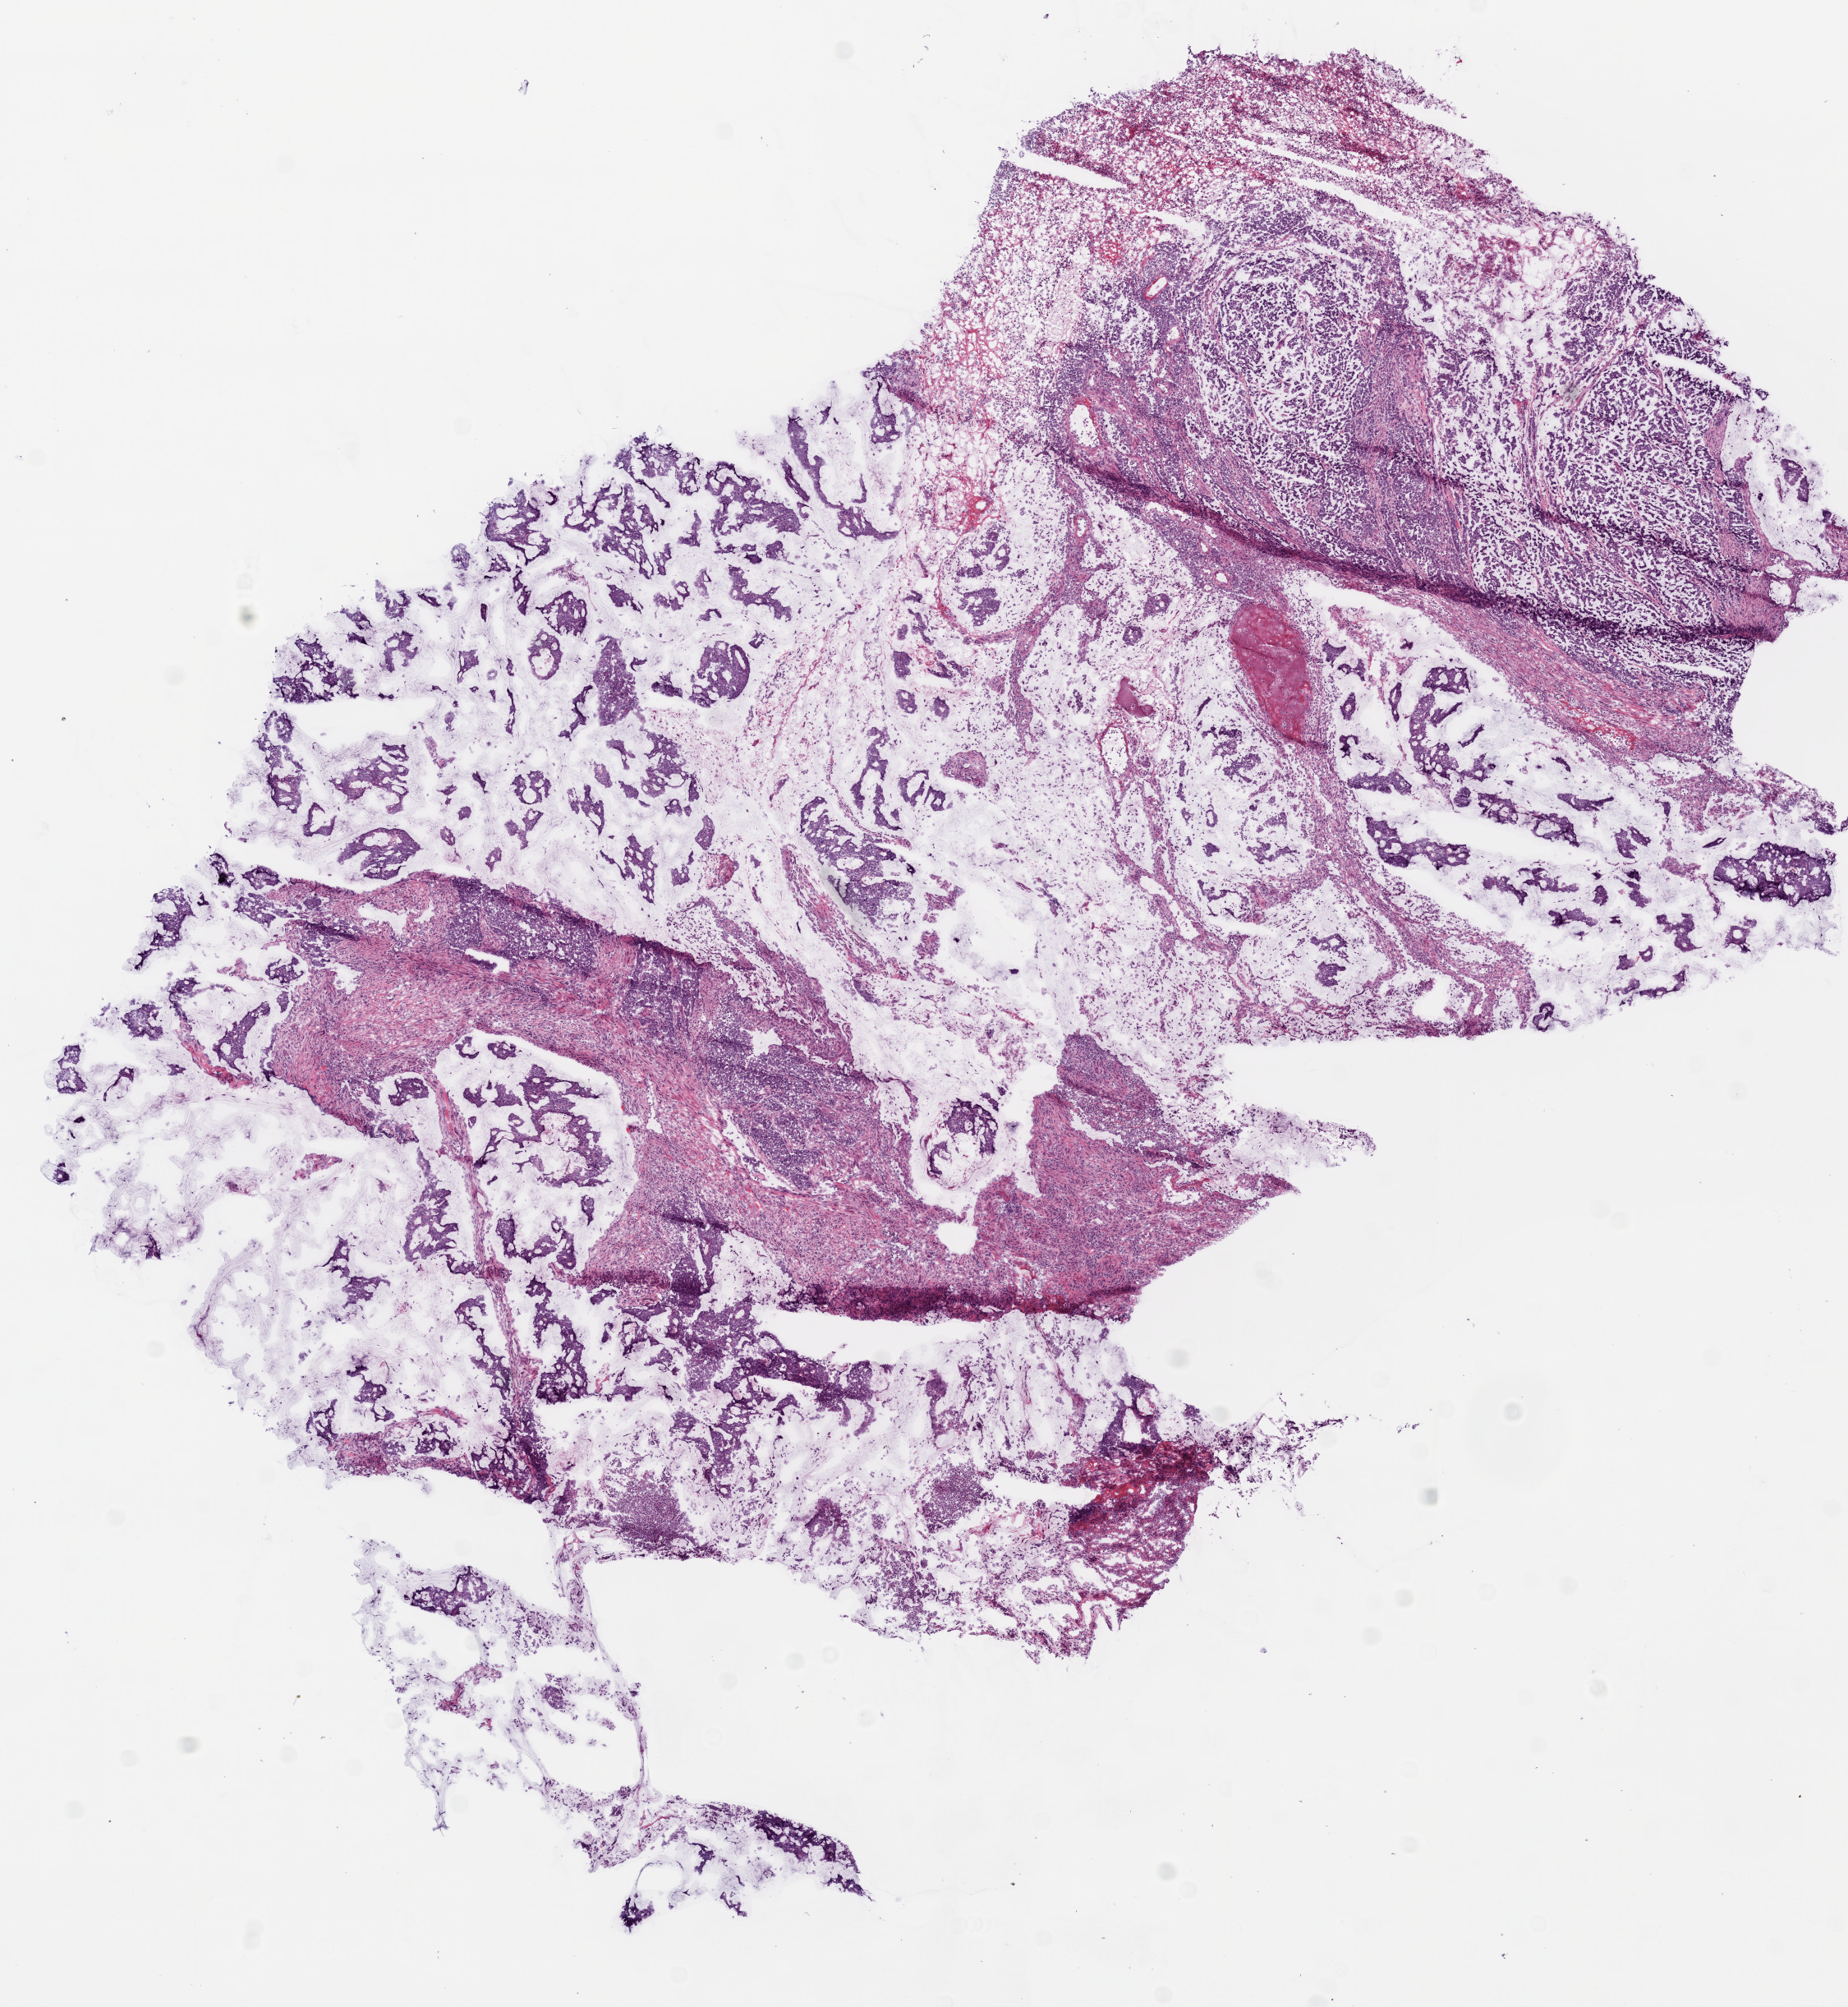
Digitized H&E-stained tissue section (whole slide), shown as a low-resolution overview of the whole scanned area (about 9.0 x 9.8 mm). Frozen section. Colon, primary tumour sample. Patient: female, age at initial diagnosis 79 years. Composition of this section per pathologist review: tumour cells 70%, tumour nuclei 70%, normal cells 0%, stromal cells 20%, necrosis 10%.
- TNM: T3 N0 M0
- histologic diagnosis: Mucinous adenocarcinoma (ascending colon)
- AJCC pathologic stage: IIA (6th edition)